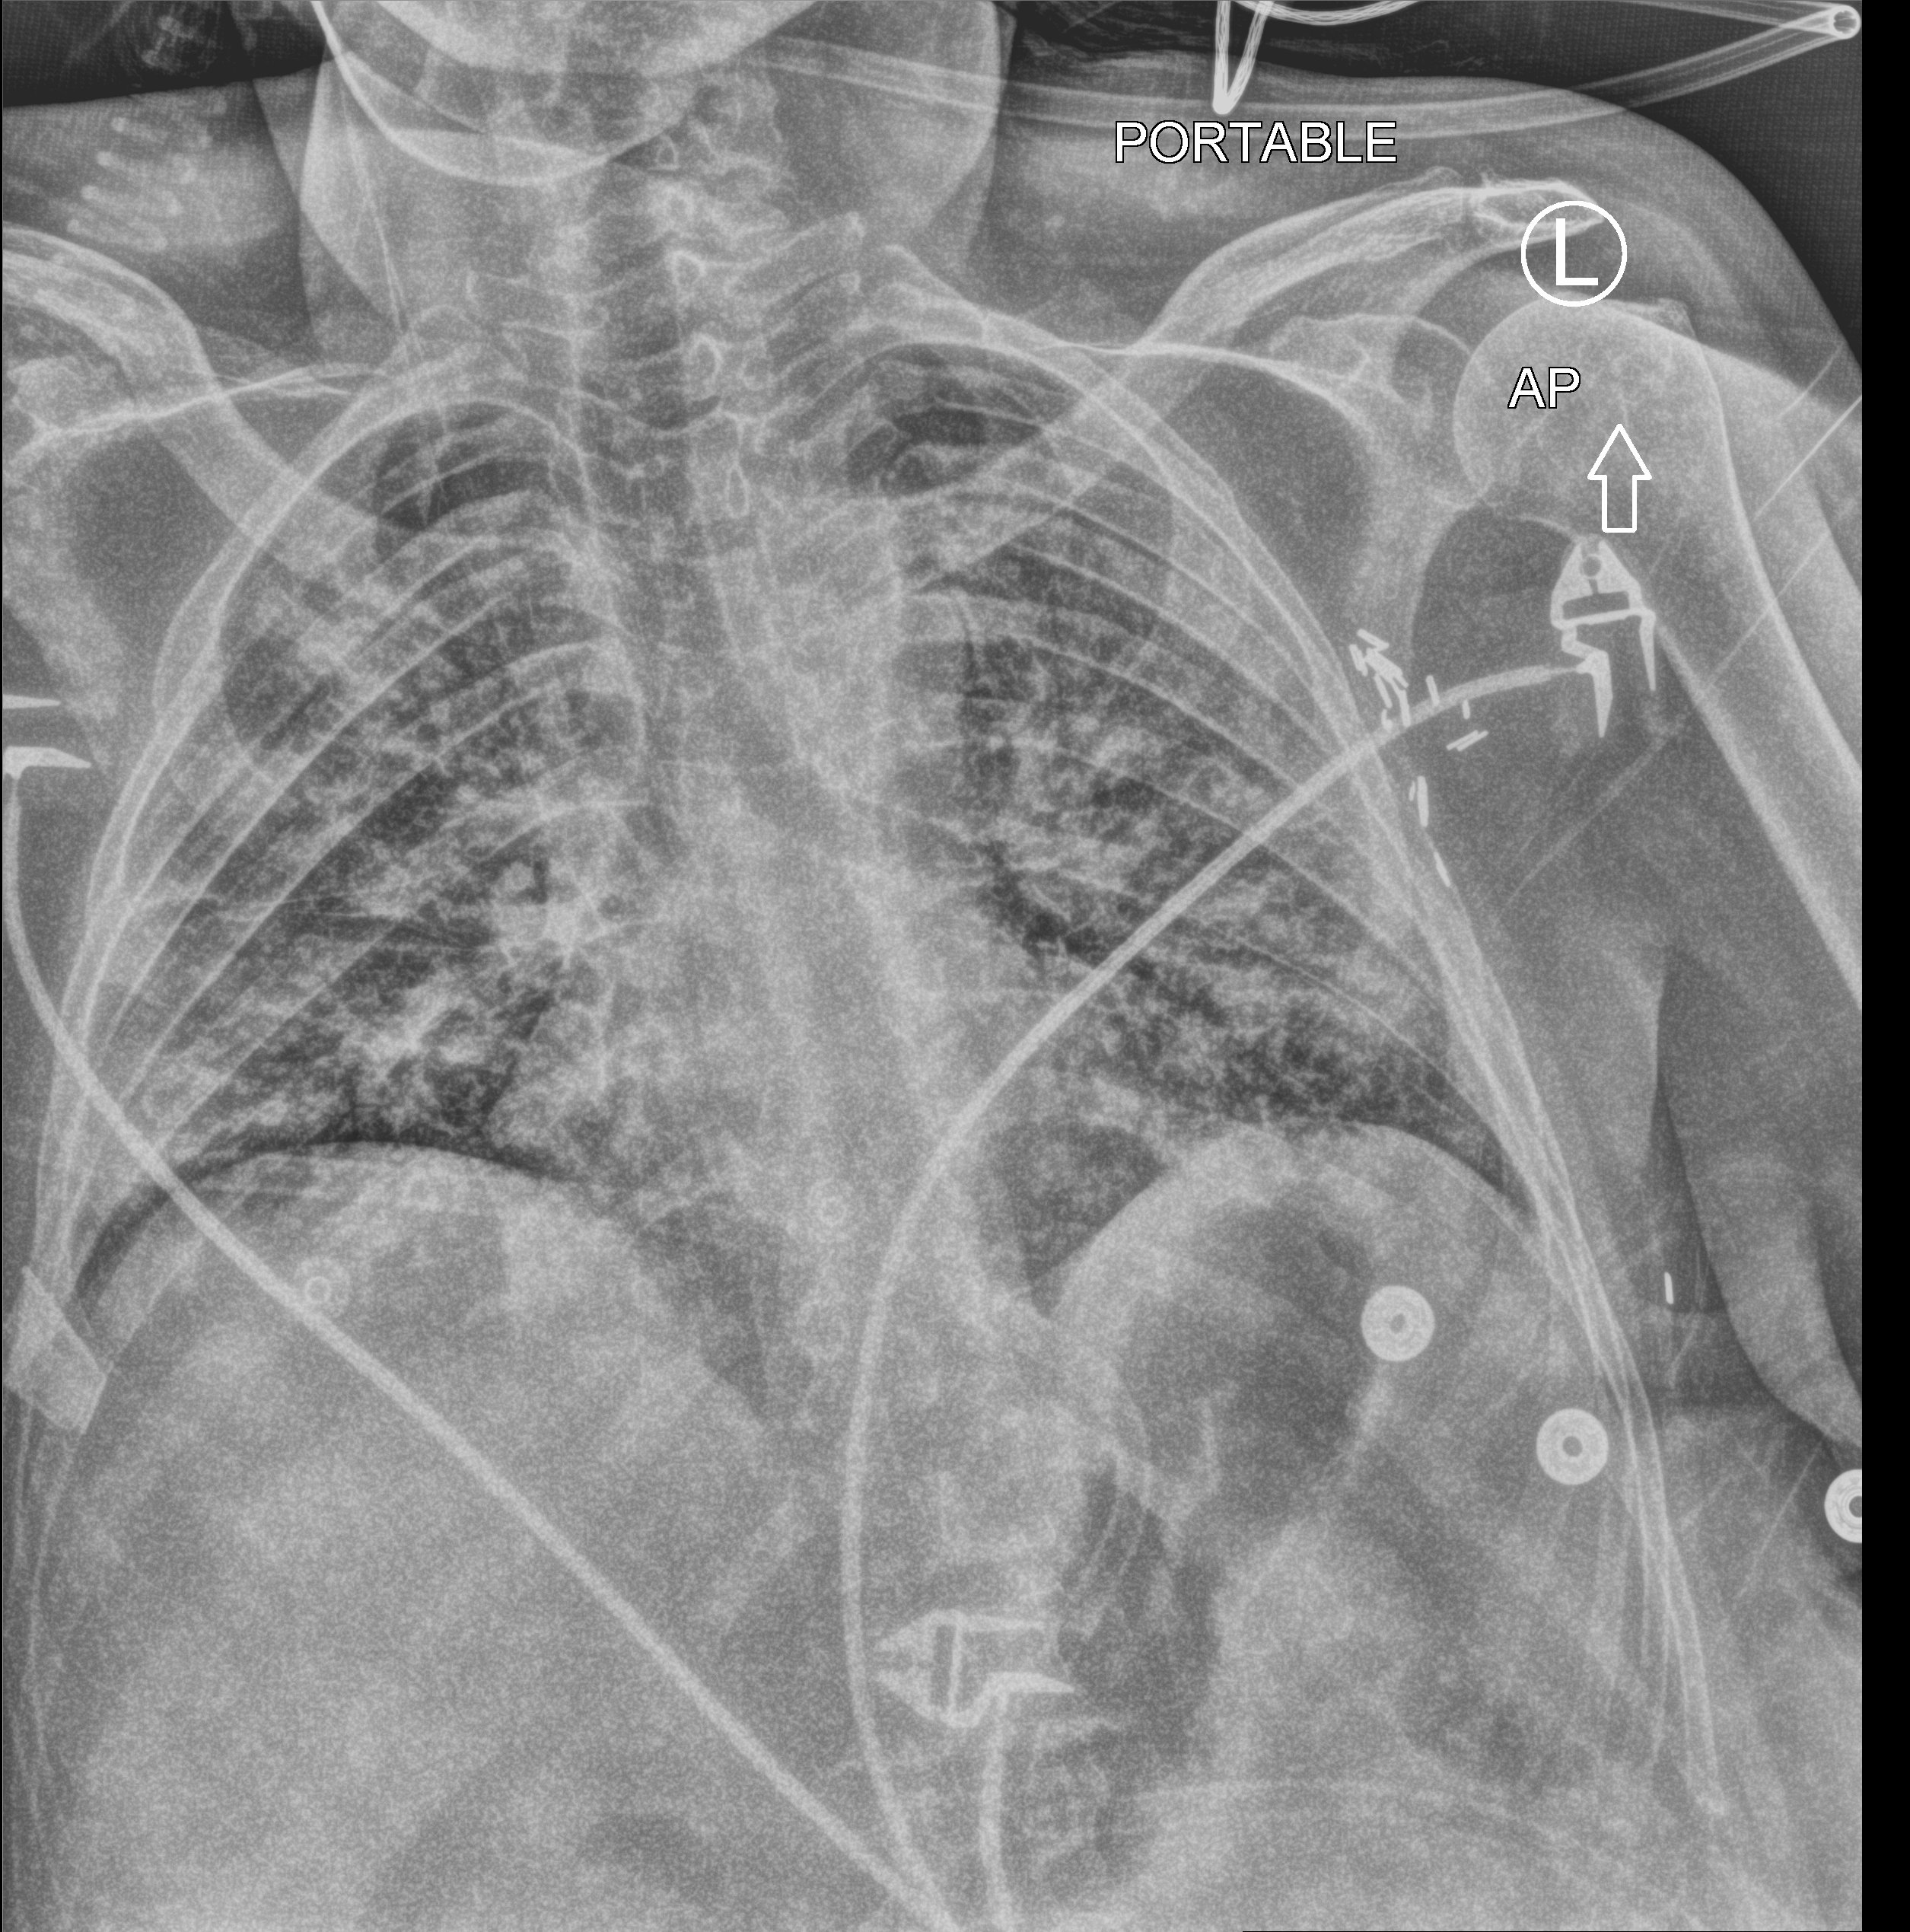
Bedside chest radiograph (computed radiography); anteroposterior (AP) projection. Female patient hospitalised with COVID-19, age 60–74 years.
From the hospital-stay record, not from the radiograph (when in the stay this image was taken is not recorded):
- smoking status (admission record): never
- other chronic lung disease (admission record): no
- length of hospital stay: 16 days